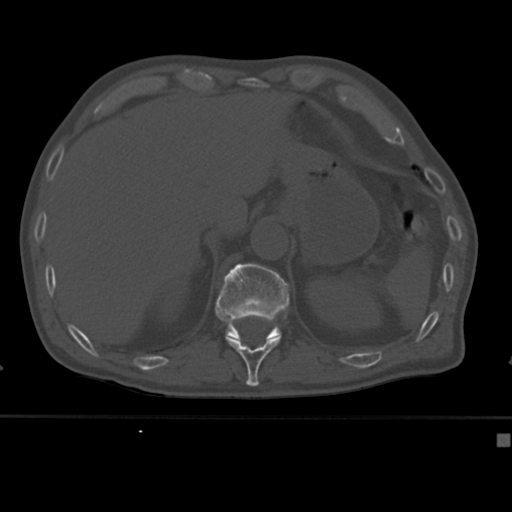
CT including the spine, one axial slice. Slice 201 of 430 in the series (ordered by position). 120 kVp. Bone window (W 1800 / L 400 HU). 512 × 512 image matrix, field of view 337 × 337 mm. Patient: male, 64 years. From the clinical record (not read from this slice): primary cancer: uterus.
Annotated regions visible in this slice (semi-automatically segmented with operator editing):
- T11 vertebra: box from (x=225, y=336) to (x=281, y=382) px
- T12 vertebra: (x=215, y=263)–(x=289, y=340)